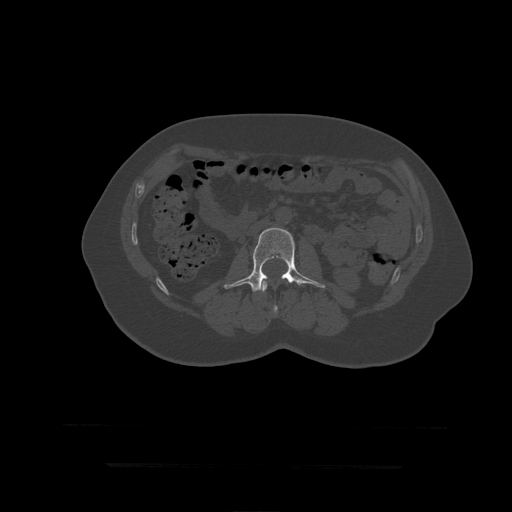
CT including the spine, one axial slice; slice 128 of 399 in the series (ordered by position); bone window (W 1800 / L 400 HU); 512 × 512 image matrix, field of view 450 × 450 mm. Patient age 41 years. From the clinical record (not read from this slice): primary cancer: breast.
Structures marked on this image (semi-automatic segmentation, software-assisted and operator-edited):
- L2 vertebra: bounding box <262,281,278,313> (left, top, right, bottom; pixels)
- L3 vertebra: <224,228,326,293>